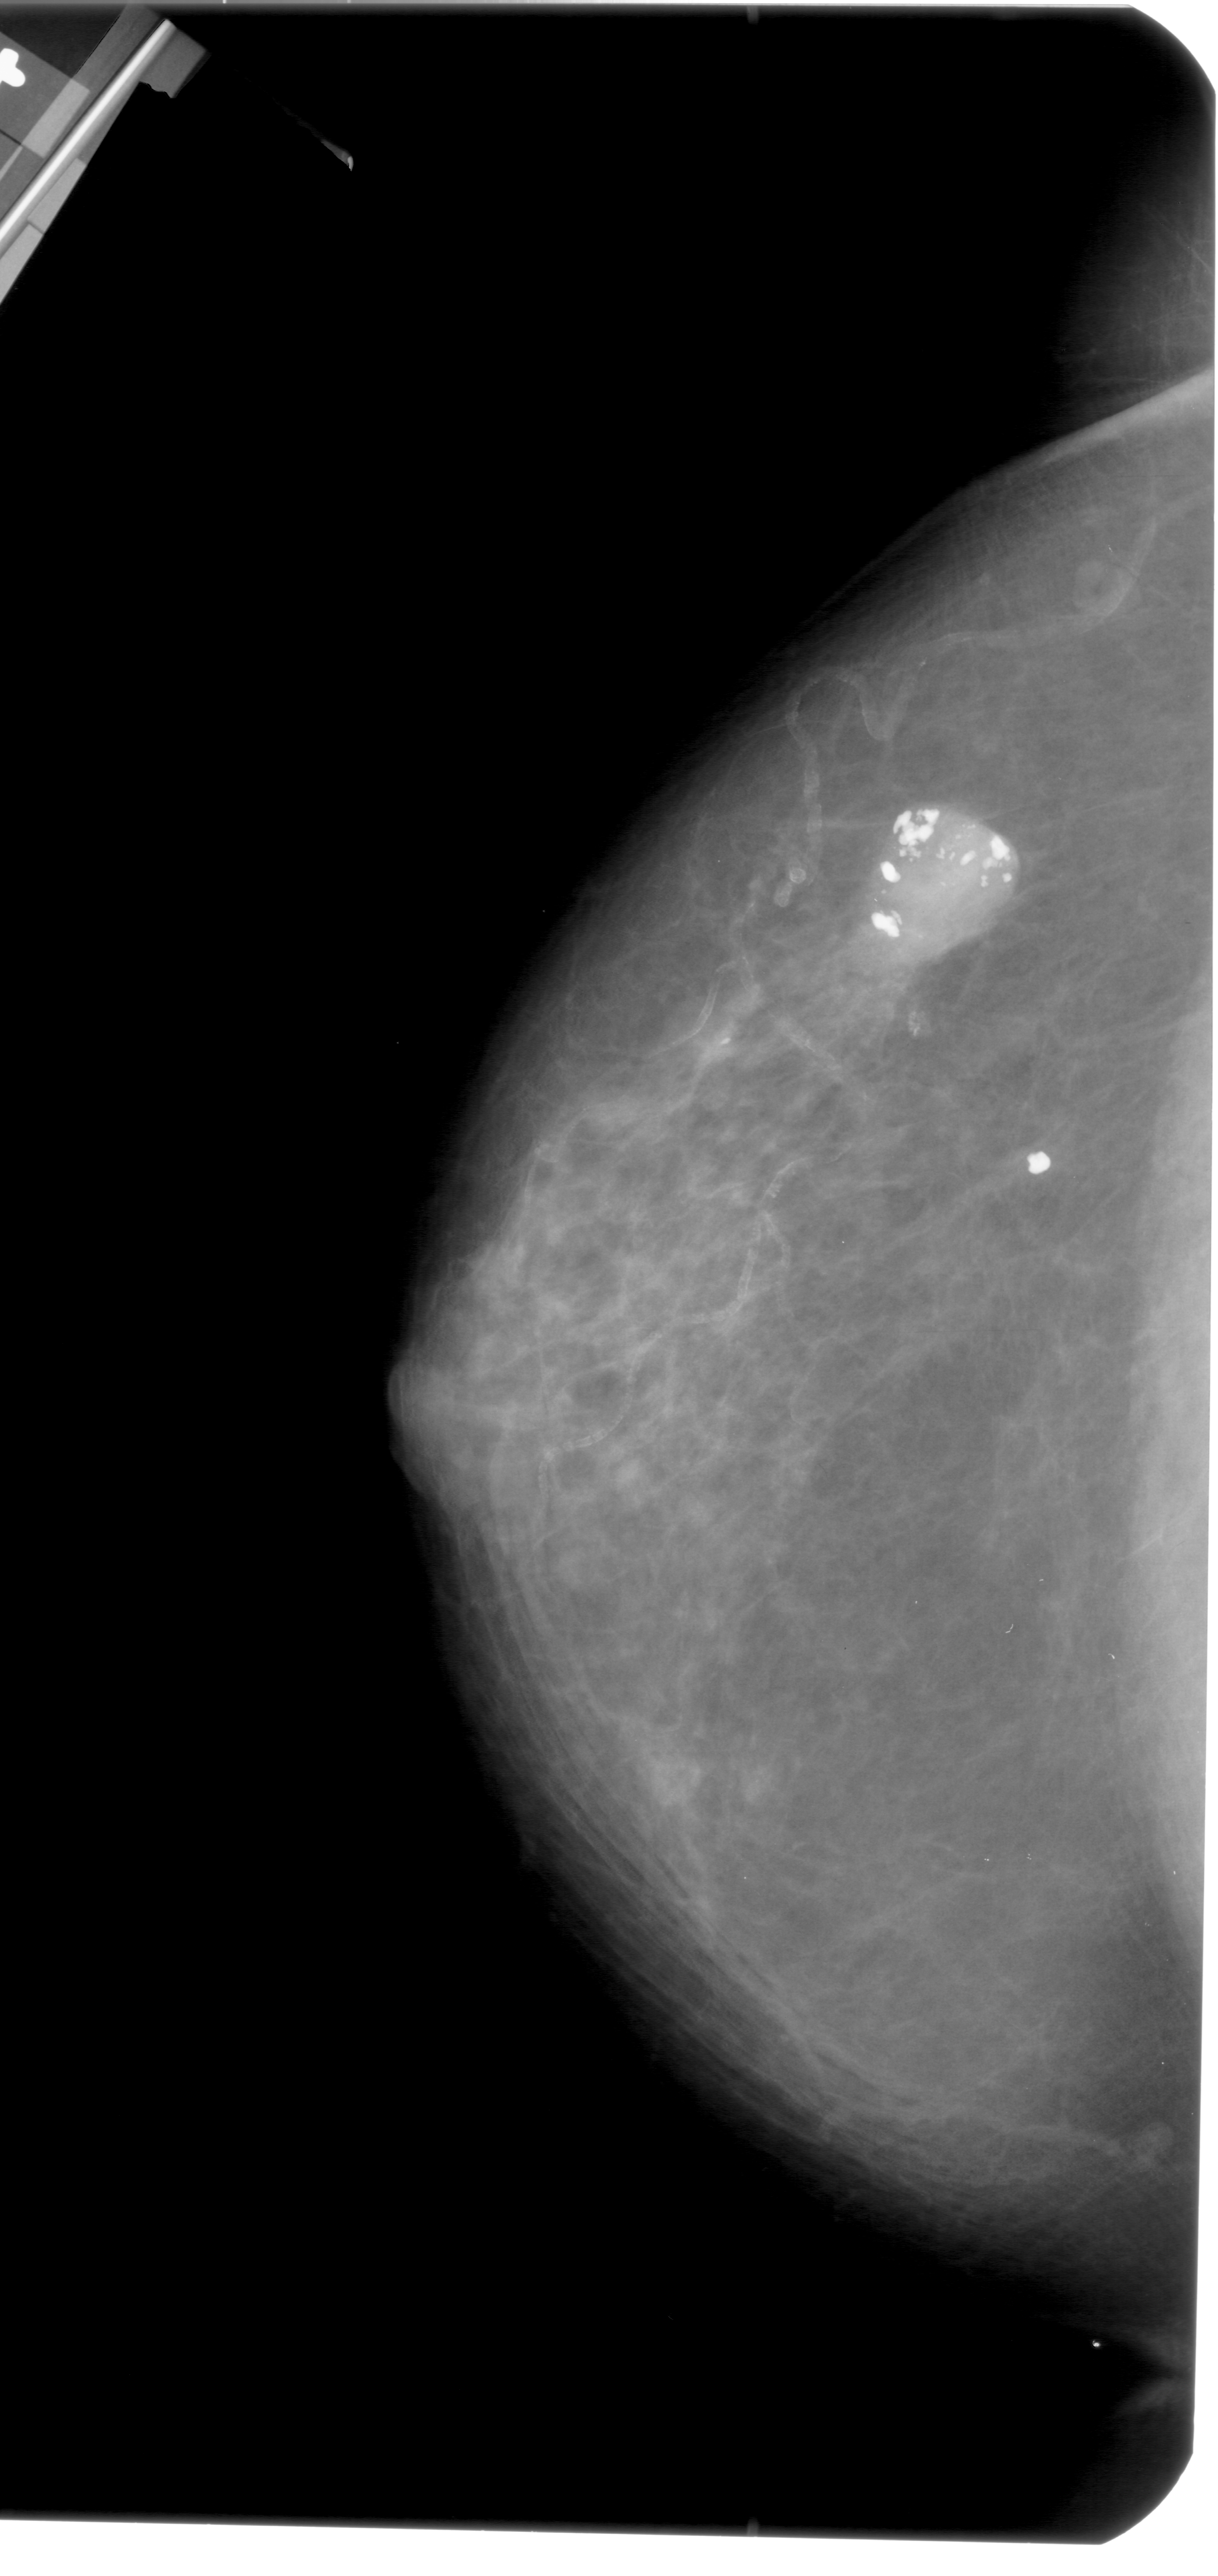
Scanned film-screen mammogram. Left breast. CC view. 1218 × 2576 image matrix.
Expert-marked regions of interest on this image (one box per marked abnormality):
- calcifications, morphology amorphous; BI-RADS assessment category 2; subtlety rating 5 on a 1 (subtle) to 5 (obvious) scale; pathology result (as recorded, not read from the image): benign: bounding box [x1, y1, x2, y2] px = [751, 729, 1087, 1080]